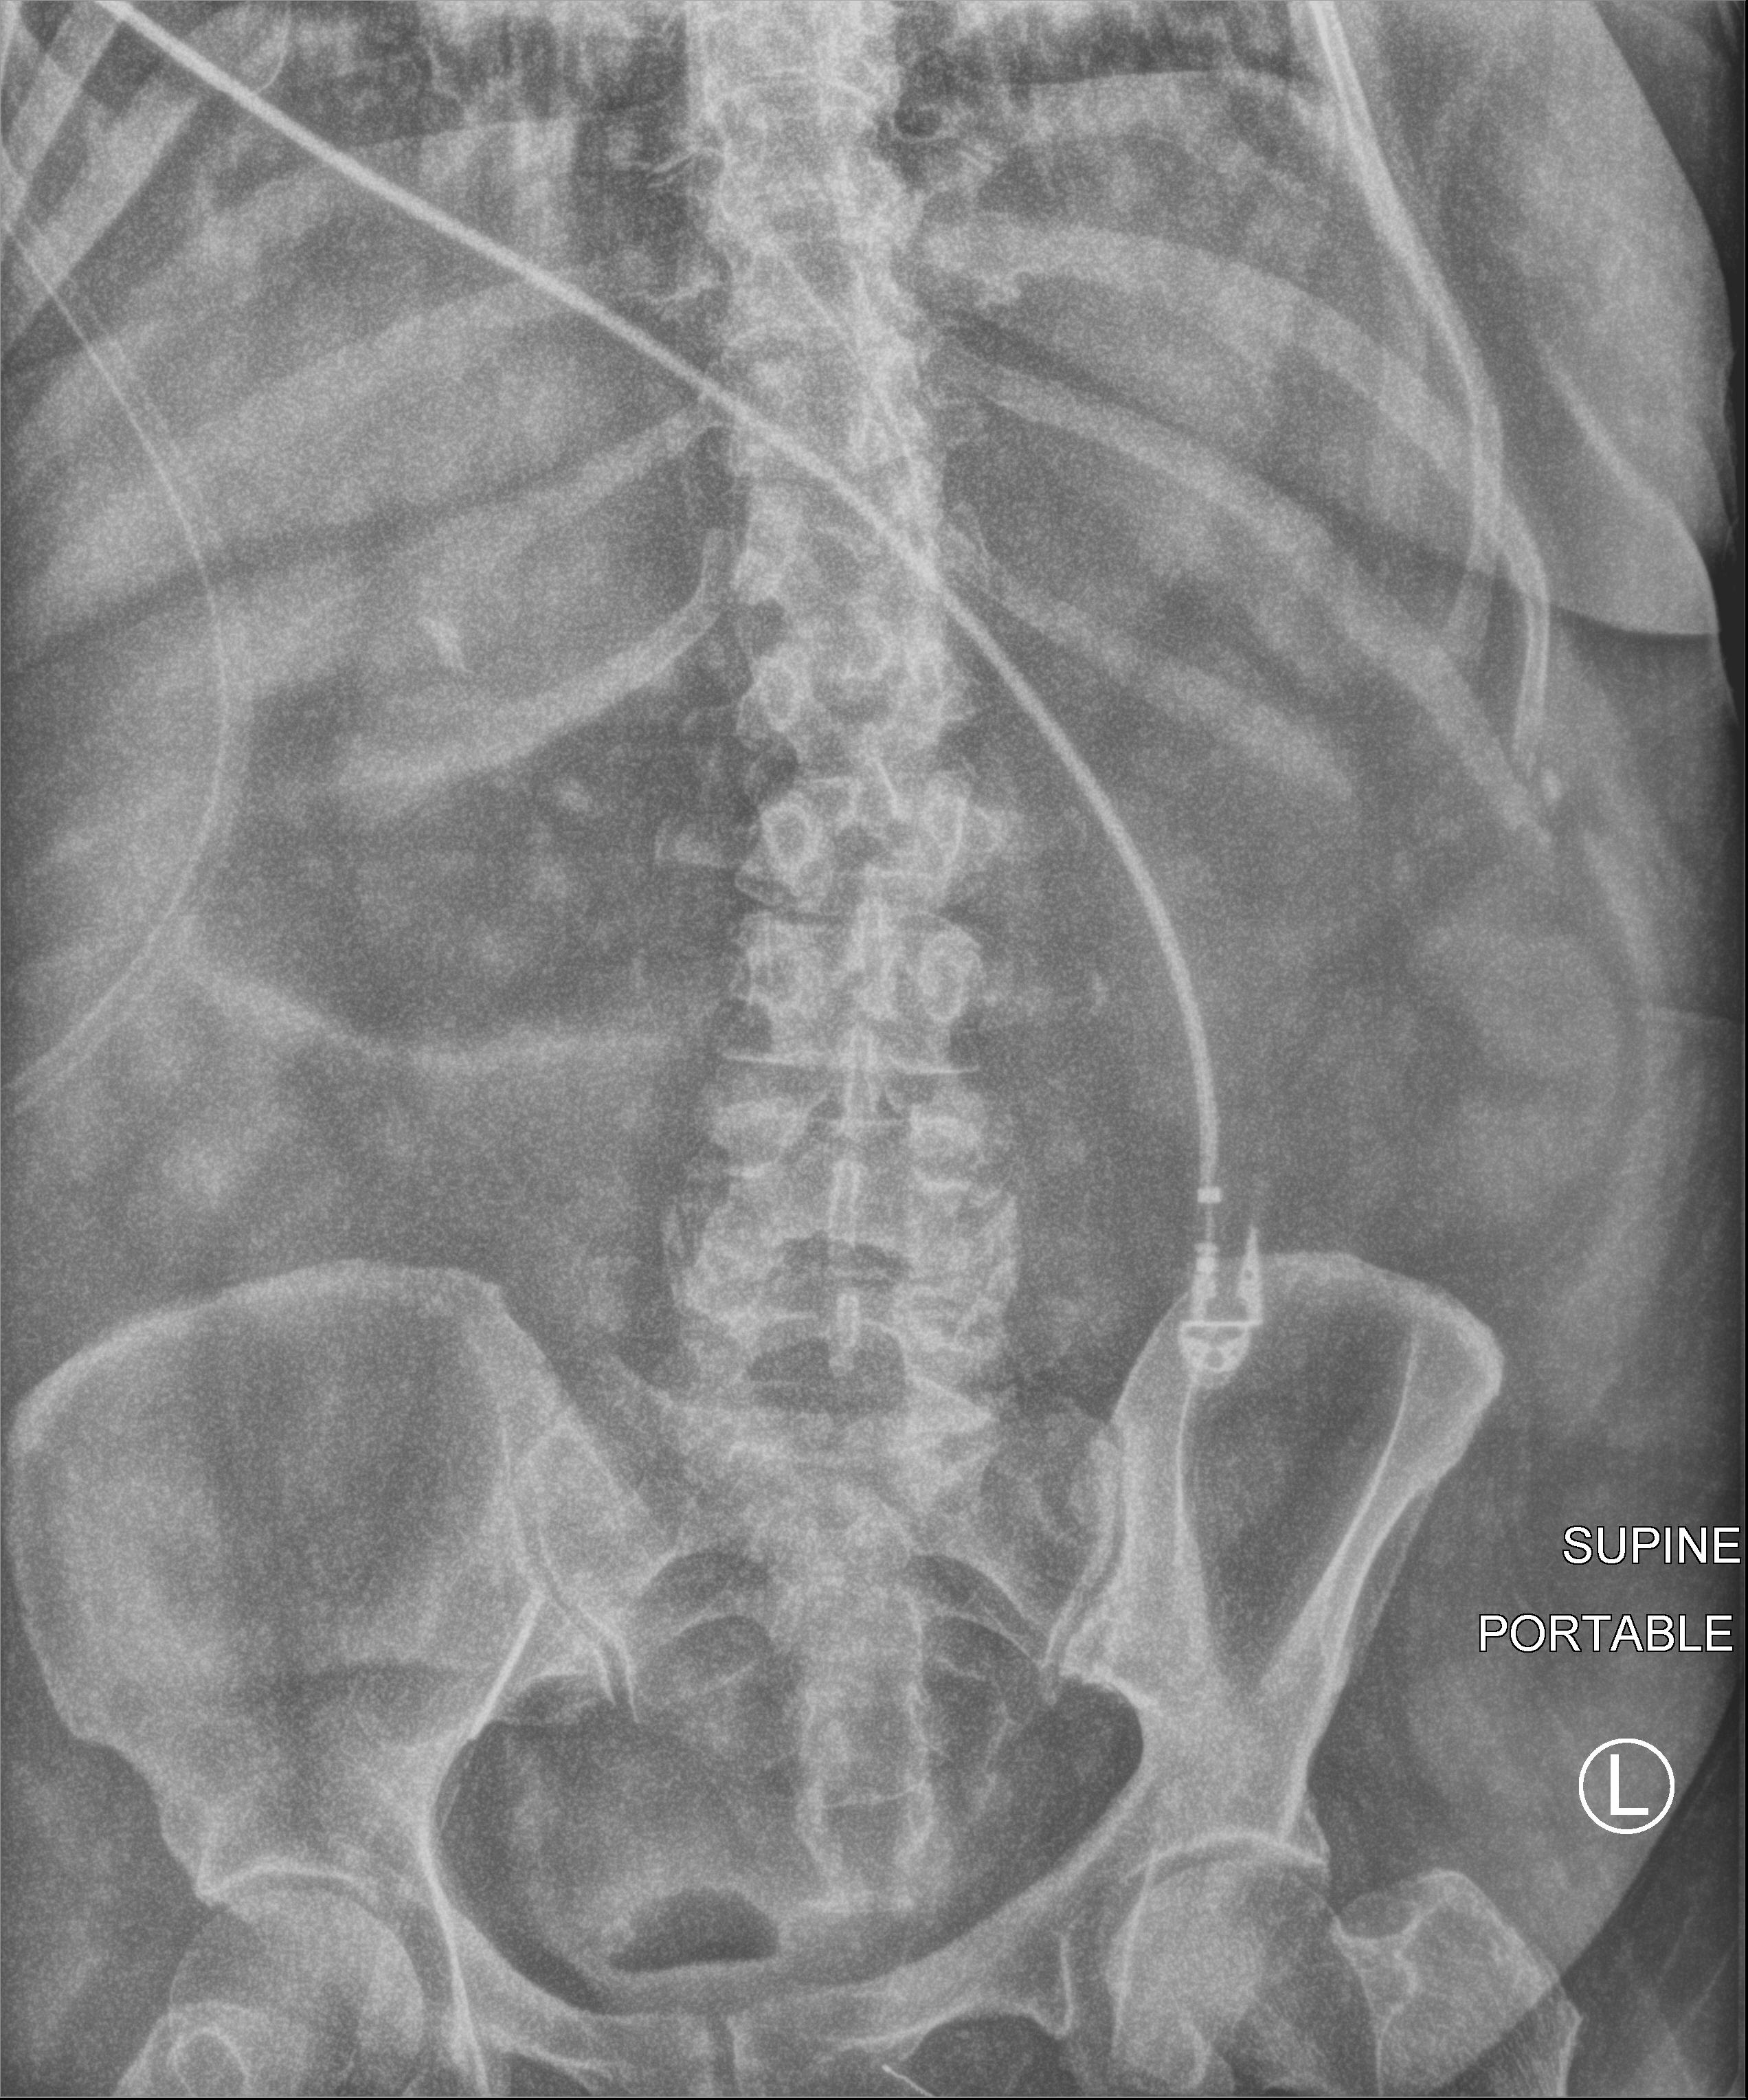
Bedside abdomen radiograph (computed radiography); anteroposterior (AP) projection. Patient hospitalised with COVID-19; female, aged 60–74 years.
Hospital-stay facts (about this admission, not read from this image; timing relative to this image not recorded): length of hospital stay: 45 days; mechanically ventilated during this hospital stay: yes.